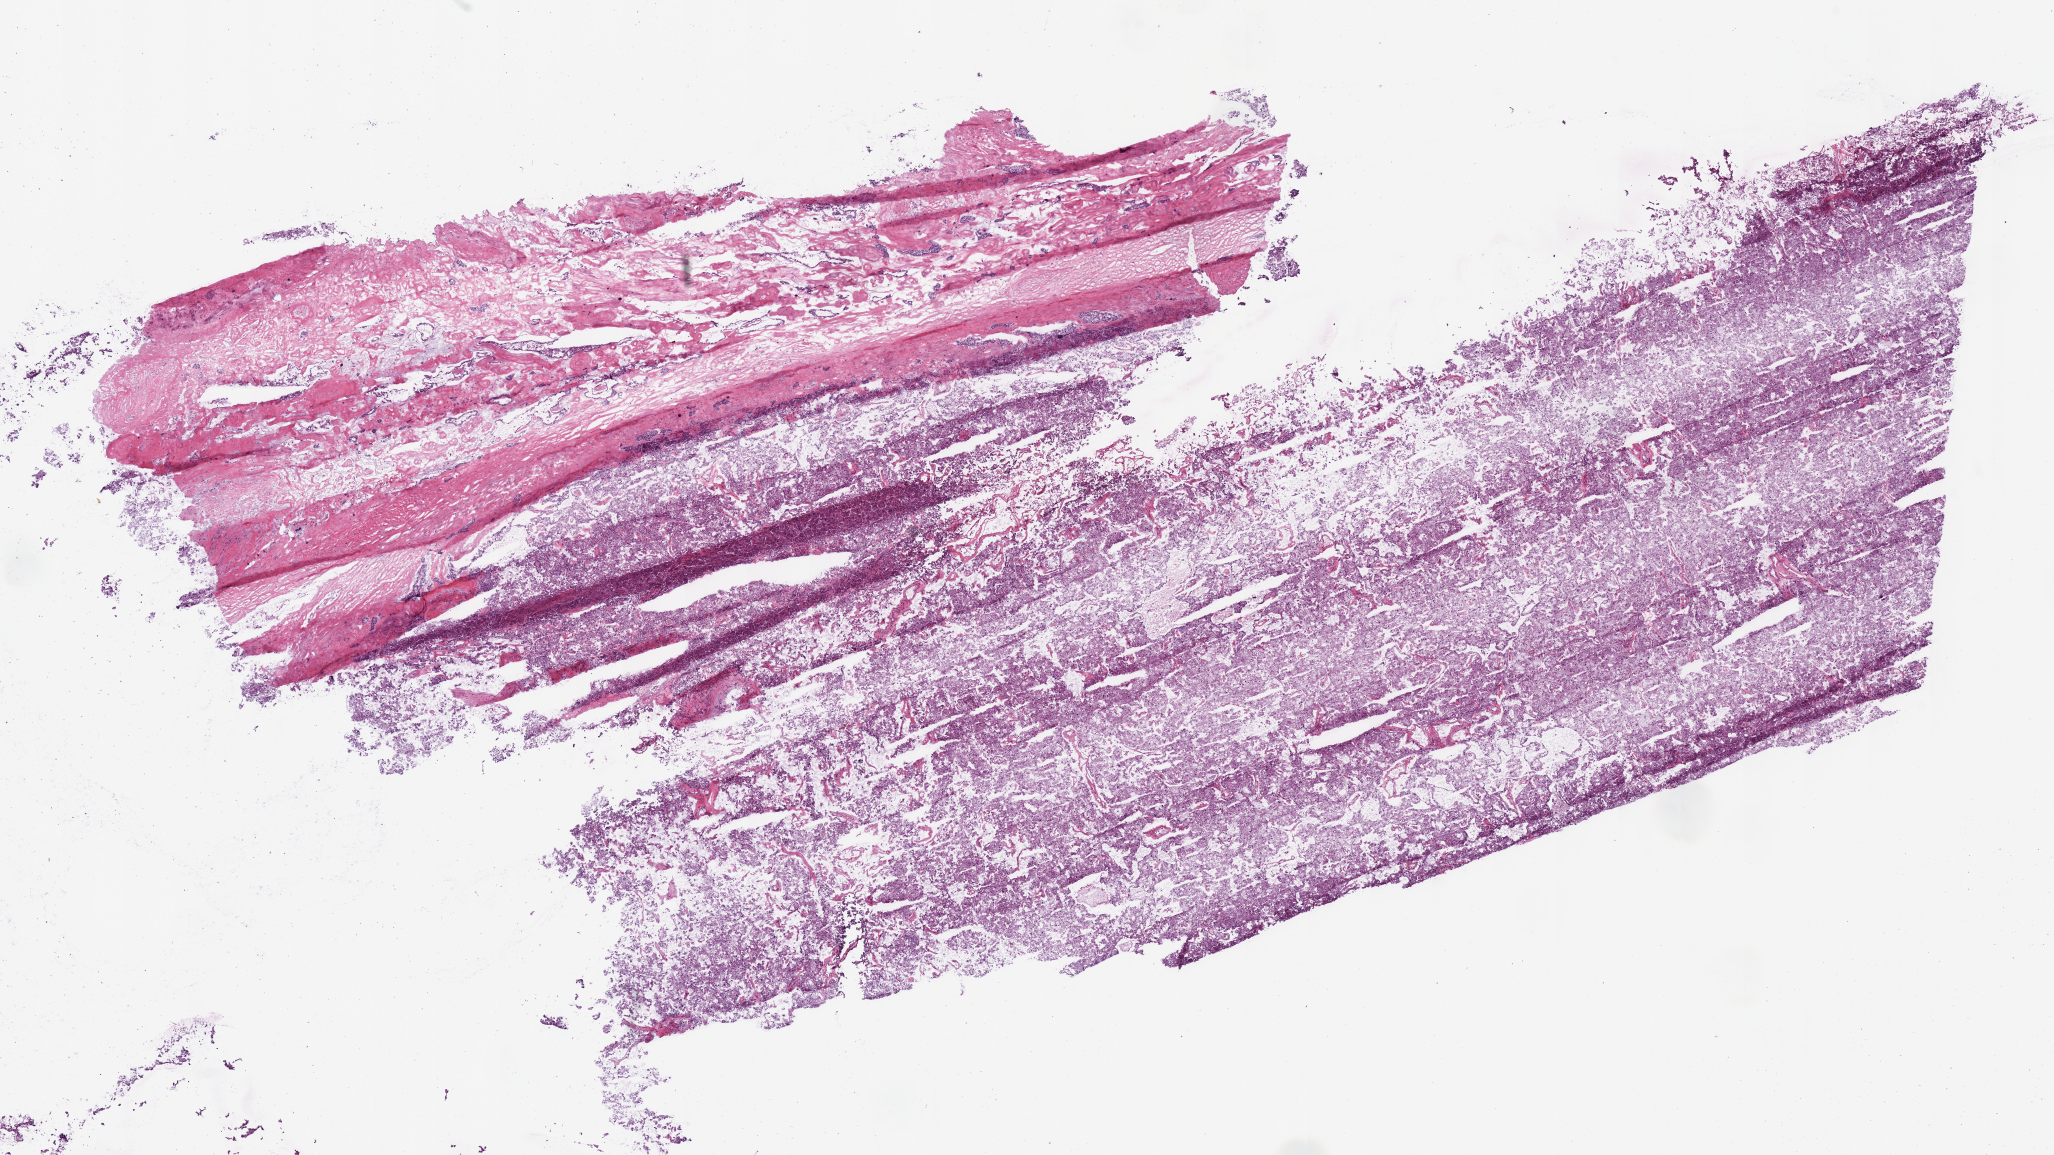
Whole-slide histology image, H&E-stained, a low-resolution overview of the entire scanned area, about 16.2 x 9.1 mm. Frozen section from the bottom of the tissue portion. Sample: primary tumour, kidney. Female patient; age at initial diagnosis 37 years. Slide review estimates, as recorded: tumour cells 80%, tumour nuclei 85%, normal cells 0%, stromal cells 20%, necrosis 0%. Infiltration values recorded for this section: lymphocyte infiltration 2%, monocyte infiltration 0%, neutrophil infiltration 0%.
Laterality: left. Pathologic diagnosis: Renal cell carcinoma, chromophobe type. AJCC pathologic stage: III (6th edition).